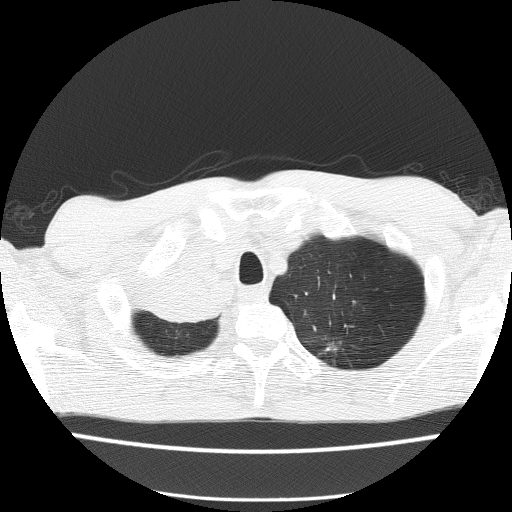
Low-dose screening chest CT, one axial slice. Position 129 of 150 along the scan axis. 120 kVp. Lung window (W 1500 / L -600 HU). 2 mm slice thickness. 512 × 512 image matrix, field of view 336 × 336 mm.
Annotated regions visible in this slice (outlined manually by an expert reader):
- lesion 1 (tumor, hilum of right lung): bounding box [x1, y1, x2, y2] px = [147, 265, 224, 322]